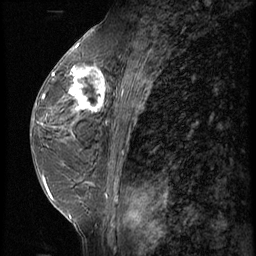
Breast MRI (dynamic contrast-enhanced), one sagittal slice. Slice 31 of 62 in the series (ordered by position). 3 images stored at this slice position (order not interpretable as contrast timing). 1.5 T. TE 4.2 ms, TR 9 ms. 256 × 256 image matrix, field of view 180 × 180 mm. Female patient, age 44 years. Case-level facts recorded for this patient, not image findings: setting: breast cancer imaged before/during neoadjuvant chemotherapy; receptor status: triple-negative.
Annotated regions visible in this slice (semi-automatically segmented with operator editing):
- analysis volume of interest (the breast-tissue region the enhancement analysis was run in; not a lesion): bounding box <67,64,116,125> (left, top, right, bottom; pixels)
- tumour enhancement mask (voxels above the 140 % enhancement threshold inside the analysis volume of interest): <68,66,108,118>